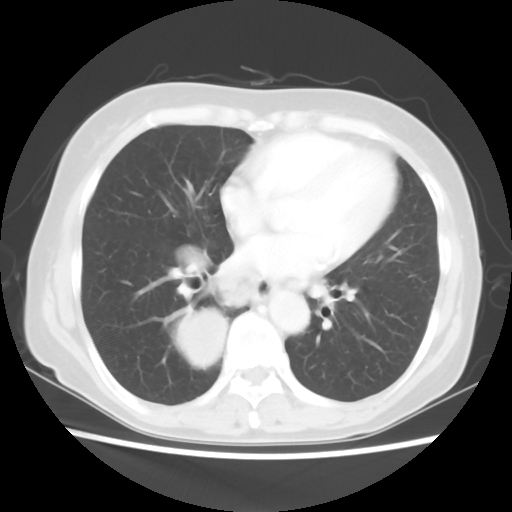
Chest CT, one axial slice. Slice 23 of 56 in the series (ordered by position). Reconstruction kernel STANDARD. Lung window (W 1500 / L -600 HU). 5 mm slice thickness. 512 × 512 image matrix, field of view 332 × 332 mm. Female patient, age 66 years. From the clinical record (not read from this slice): clinical TNM (as recorded): T2 N3 M0; histopathological grade: G3.
Structures marked on this image (rectangle marked by the reading radiologist):
- lung tumour (recorded histology: small cell carcinoma): bounding box (x1, y1, x2, y2) in pixels: (175, 303, 232, 371)